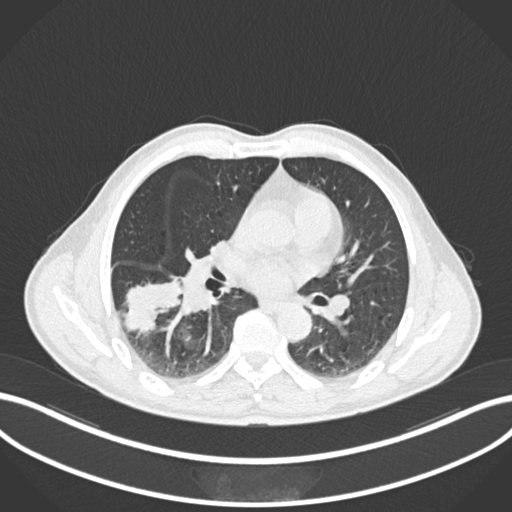
Chest CT, one axial slice. Position 99 of 208 along the scan axis. Reconstruction kernel B30f. Lung window (W 1500 / L -600 HU). 512 × 512 image matrix, field of view 400 × 400 mm. Male patient, age 58 years. From the clinical record (not read from this slice): clinical TNM (as recorded): T3 N0 M0.
Annotated regions visible in this slice (bounding box drawn by a radiologist):
- lung tumour (recorded histology: squamous cell carcinoma): bounding box [x1, y1, x2, y2] px = [118, 268, 186, 335]